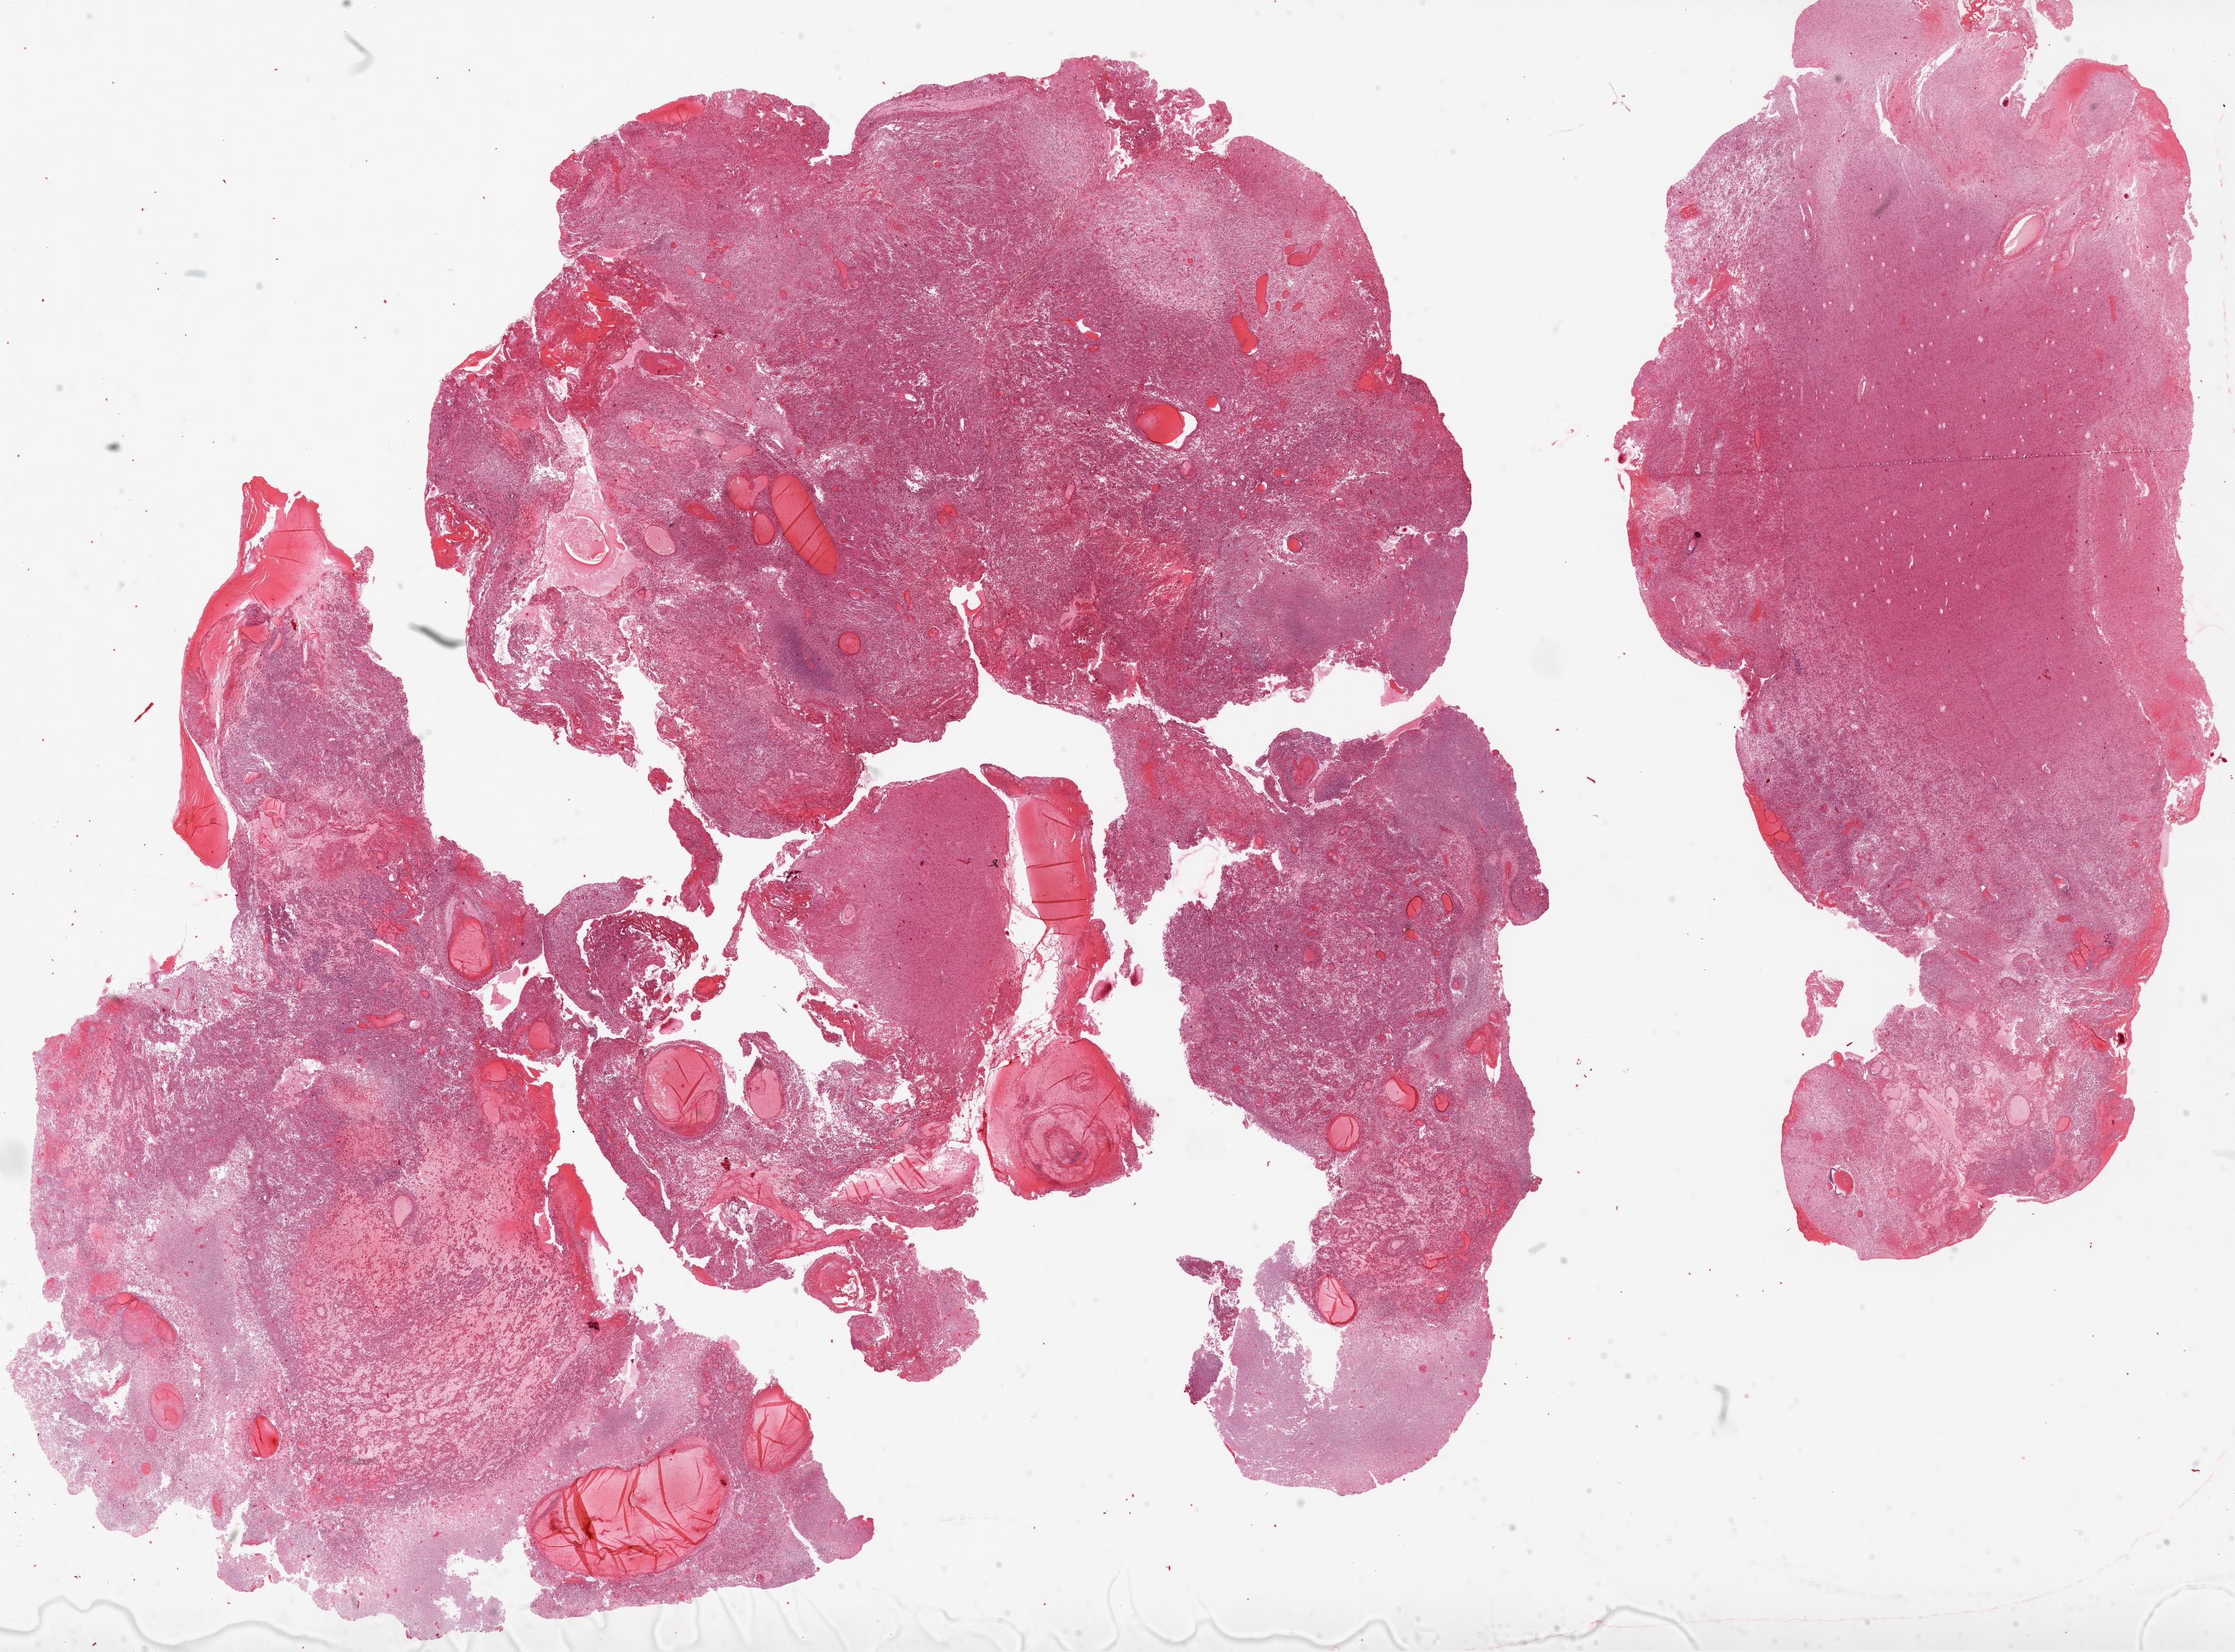
Digitized H&E-stained tissue section (whole slide), low-resolution overview of the scanned area, about 28.1 x 20.8 mm, formalin-fixed paraffin-embedded (FFPE) diagnostic section, primary tumour sample from the brain. Patient: female, age at initial diagnosis 59 years.
* diagnosis: Glioblastoma